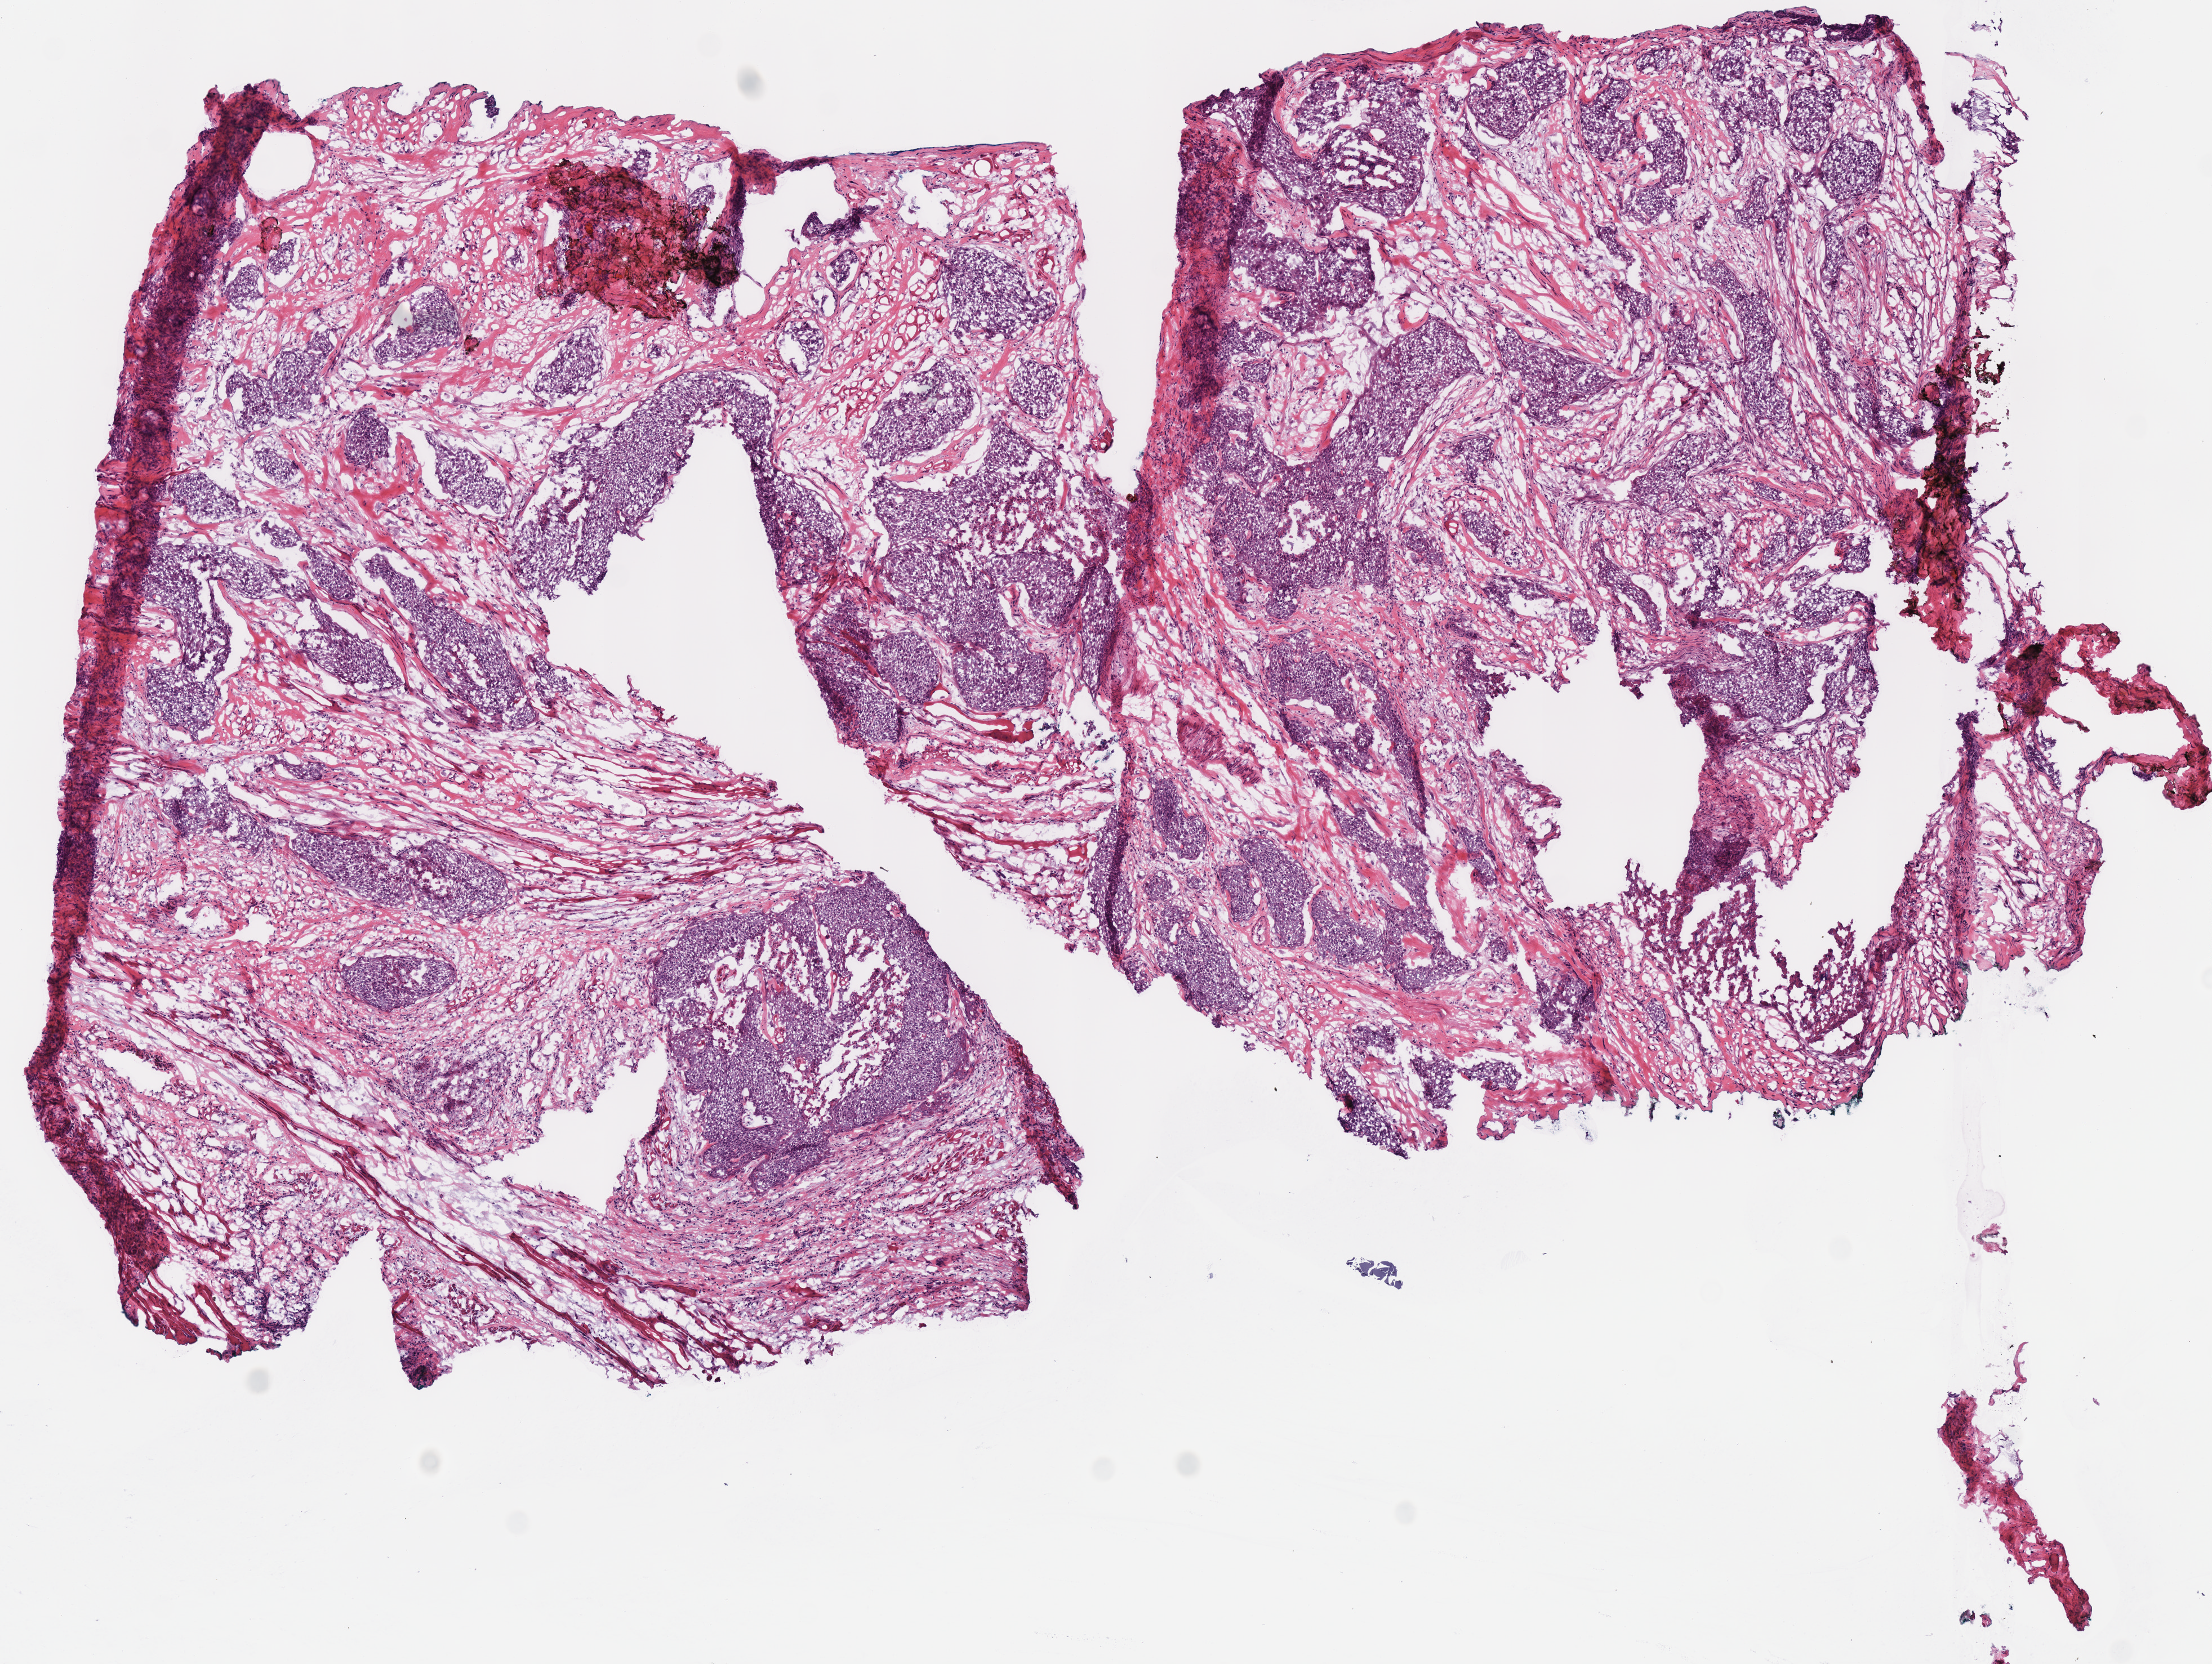
Digitized Hematoxylin and eosin (H&E) stained tissue section (whole slide) — whole scanned area (about 7.7 x 5.8 mm) shown as a low-resolution overview; frozen section from the top of the tissue portion; sample: primary tumour, head and neck. Male, age 49 years at initial diagnosis. Histologic grade: GX (grade cannot be assessed). Composition of this section per pathologist review: tumour cells 86%, tumour nuclei 73%, normal cells 0%, stromal cells 14%, necrosis 0%. Infiltration values recorded for this section: lymphocyte infiltration 5%, monocyte infiltration 0%, neutrophil infiltration 0%.
- histologic diagnosis: Squamous cell carcinoma, NOS
- AJCC pathologic stage: II (7th edition)
- TNM: T2 N0